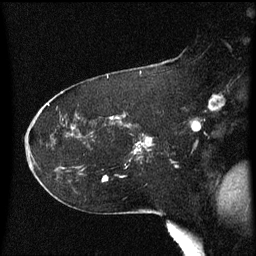
Breast MRI (dynamic contrast-enhanced), one sagittal slice. Position 37 of 60 along the scan axis. Dynamic contrast-enhanced series, image 2 of 3 at this slice position (ordered by acquisition). 1.5 T. TE 4.2 ms, TR 8.4 ms. 2 mm slice thickness. 256 × 256 image matrix, field of view 200 × 200 mm. Patient: female, 54 years. From the clinical record (not read from this slice): setting: breast cancer imaged before/during neoadjuvant chemotherapy; receptor status: HR-positive, HER2-negative.
Structures marked on this image (semi-automatically segmented with operator editing):
- analysis volume of interest (the breast-tissue region the enhancement analysis was run in; not a lesion): bounding box [x1, y1, x2, y2] px = [121, 122, 154, 155]
- tumour enhancement mask (voxels above the 70 % enhancement threshold inside the analysis volume of interest): [141, 138, 151, 143]